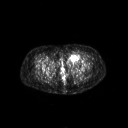
FDG PET of an extremity soft-tissue mass (from a PET/CT study), one axial slice. 3.27 mm slice thickness. 128 × 128 image matrix, field of view 700 × 700 mm. Patient: female, 47 years. From the clinical record (not read from this slice): histological type: myxofibrosarcoma; grade: intermediate; site of the primary tumour: left thigh.
Outlined on this slice (expert contour drawn on MRI and transferred to this co-registered scan by the dataset authors):
- gross tumour volume including surrounding oedema: bounding box [x1, y1, x2, y2] px = [65, 53, 83, 64]
- gross tumour volume (mass): [67, 53, 80, 62]